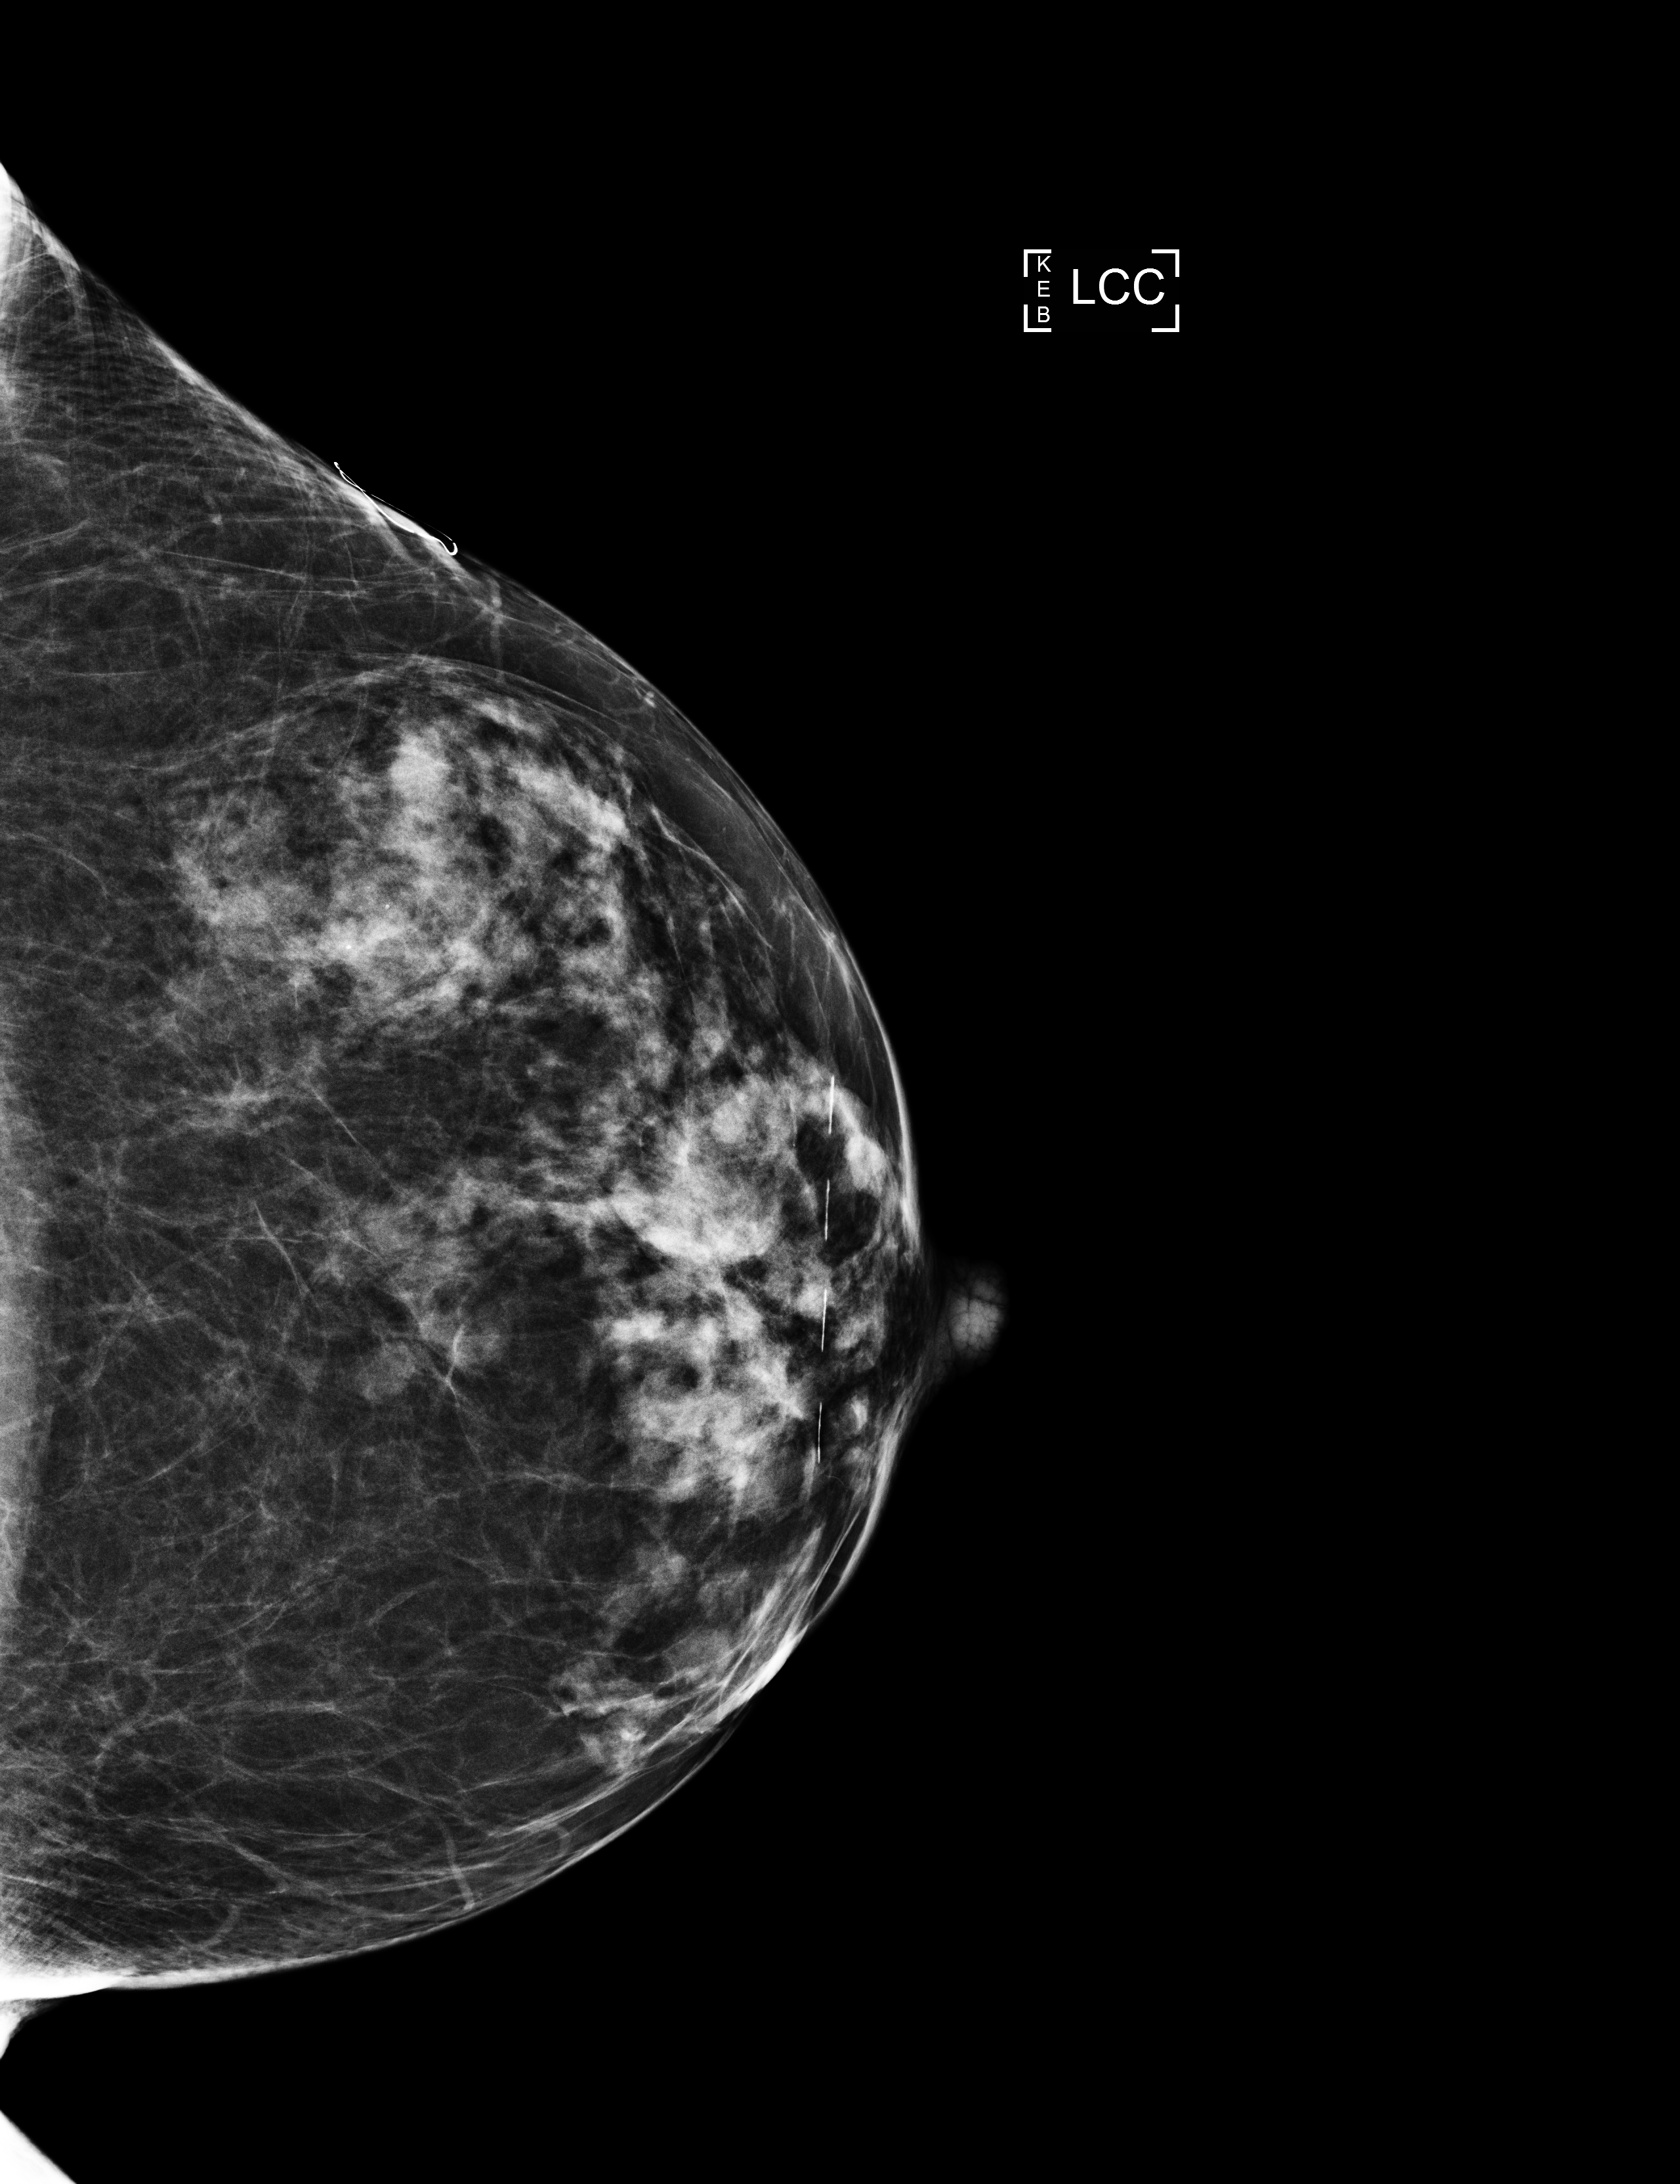
Screening examination, compressed breast thickness 53 mm. Patient: female, 72 years.
Image type: full-field digital mammogram. Breast: left. Projection: craniocaudal (CC) view. BI-RADS breast density category at the screening exam (both breasts, scale 1–4): 3. Final BI-RADS category for the screening round (tomosynthesis exam, both breasts): category 1. Recall: no recall after this screen.